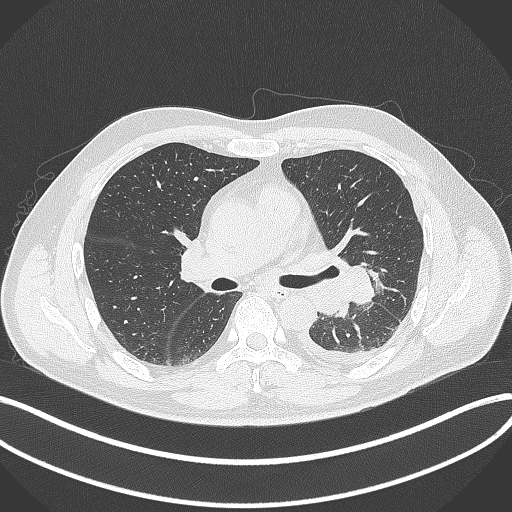
Chest CT, one axial slice; slice 210 of 342 in the series (ordered by position); 120 kVp; lung window (W 1500 / L -600 HU); 512 × 512 image matrix. Male patient, age 58 years. From the clinical record (not read from this slice): clinical TNM (as recorded): T3 N1 M1b.
Outlined on this slice (rectangle marked by the reading radiologist):
- lung tumour (recorded histology: small cell carcinoma): bounding box [x1, y1, x2, y2] px = [344, 264, 376, 308]